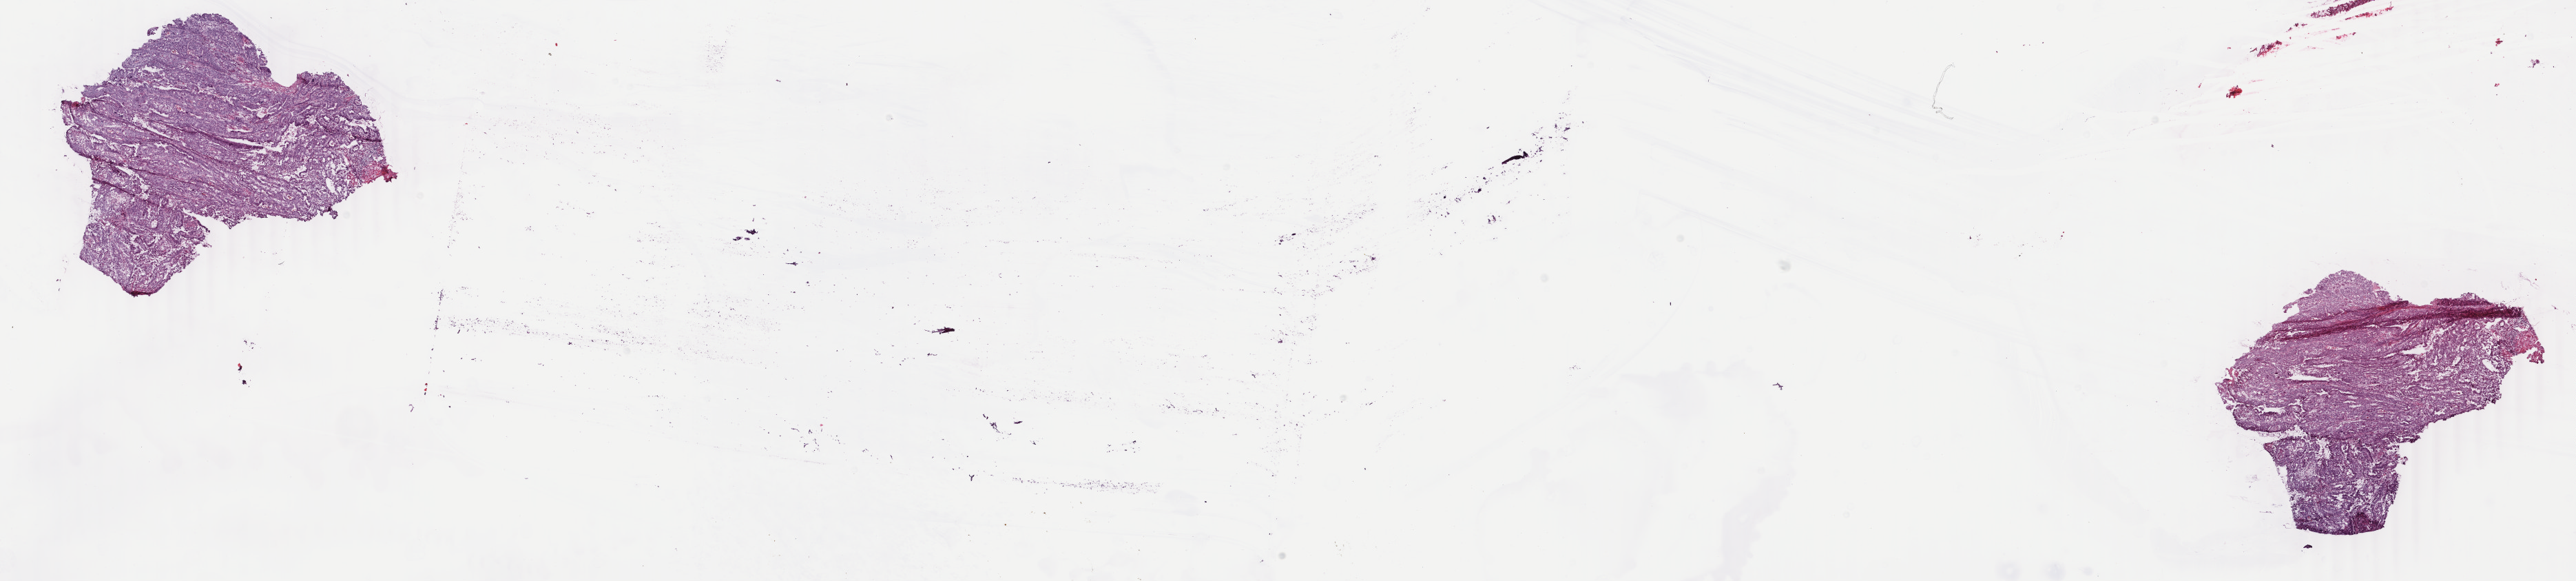
H&E whole-slide image — a low-resolution overview of the entire scanned area, about 29.7 x 6.7 mm (from a 40x scan). Frozen section. Sample: primary tumour, rectum. Male, age 35 years at initial diagnosis. Pathologist review of this section (percent, as recorded): tumour cells 95%, tumour nuclei 95%, normal cells 0%, stromal cells 4%, necrosis 1%. Inflammatory infiltration, as recorded: lymphocyte infiltration 1%, monocyte infiltration 1%, neutrophil infiltration 0%.
• lymph nodes positive (case pathology): 0 of 34 examined
• AJCC pathologic stage: I (6th edition)
• pathologic diagnosis: Adenocarcinoma, NOS